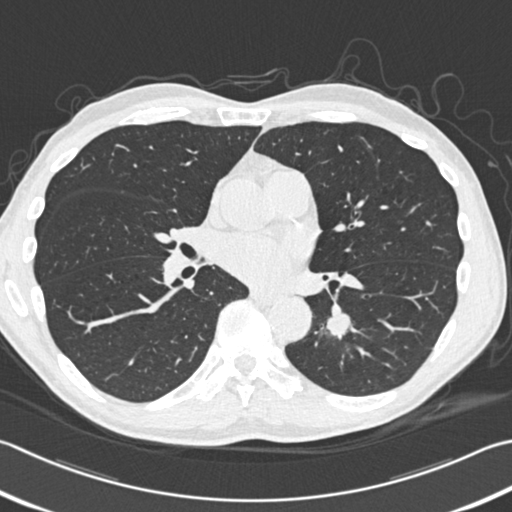
Low-dose screening chest CT, one axial slice. Slice 176 of 354 in the series (ordered by position). Reconstruction kernel B30f. 120 kVp. Lung window (W 1500 / L -600 HU). 1 mm slice thickness. 512 × 512 image matrix.
Annotated regions visible in this slice (manually delineated by an expert):
- lesion 1 (tumor, lower lobe of left lung): bounding box (x1, y1, x2, y2) in pixels: (326, 314, 351, 337)